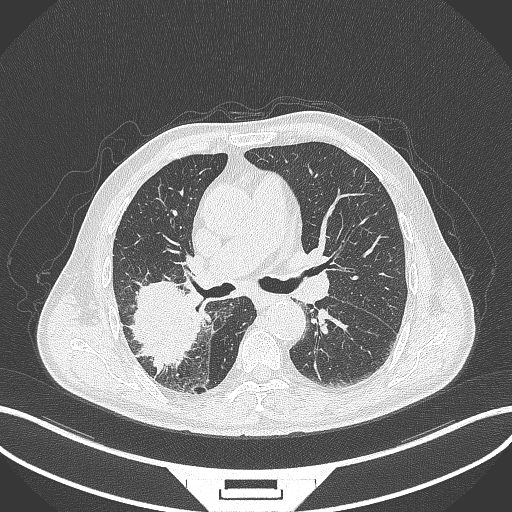
Chest CT, one axial slice; slice 241 of 429 in the series (ordered by position); 120 kVp; lung window (W 1500 / L -600 HU); 512 × 512 image matrix, field of view 400 × 400 mm. Male patient, age 72 years. Case-level facts recorded for this patient, not image findings: clinical TNM (as recorded): T3 N2 M0.
Structures marked on this image (bounding box drawn by a radiologist):
- lung tumour (recorded histology: adenocarcinoma): bounding box [x1, y1, x2, y2] px = [125, 276, 203, 371]